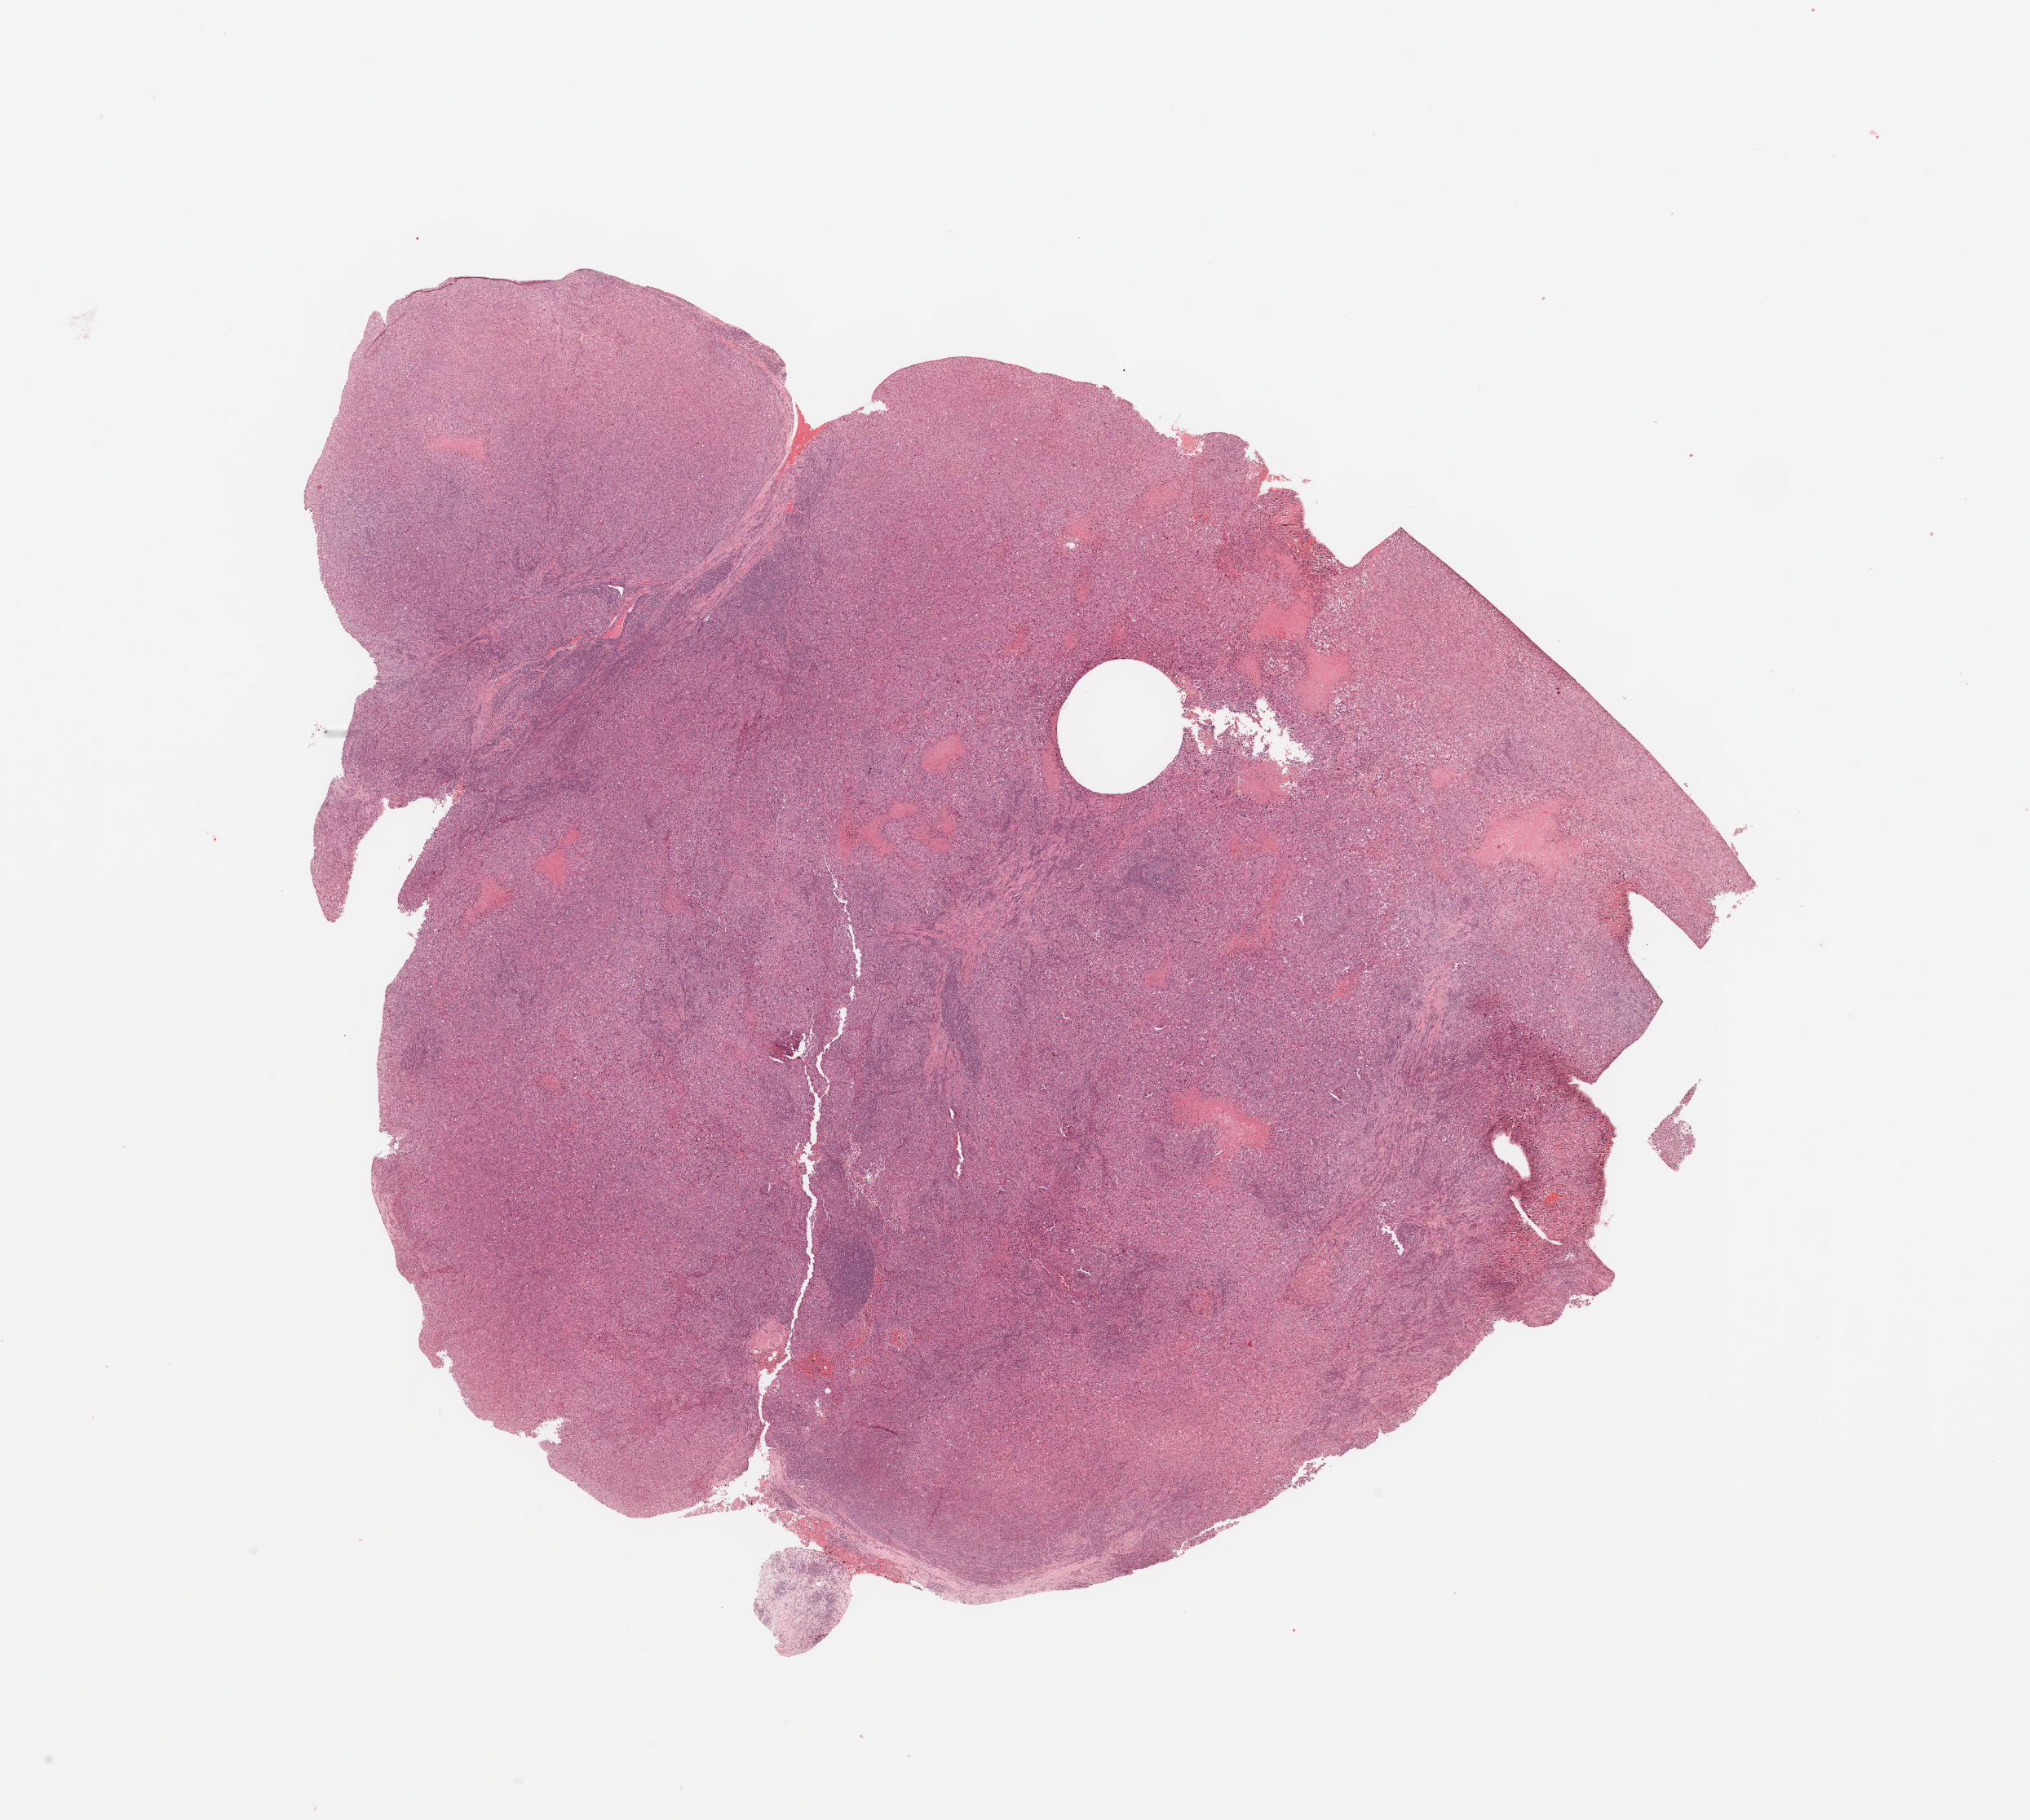
Digitized Hematoxylin and eosin (H&E) stained tissue section (whole slide) — a low-resolution overview of the entire scanned area, about 19.7 x 17.7 mm (slide scanned at 20x); tumour tissue sample. Patient: male, age 86 years.
Patient diagnosis (cohort enrolment): sarcoma (site not recorded at cohort level). Primary tumour site (as recorded): lower extremity.